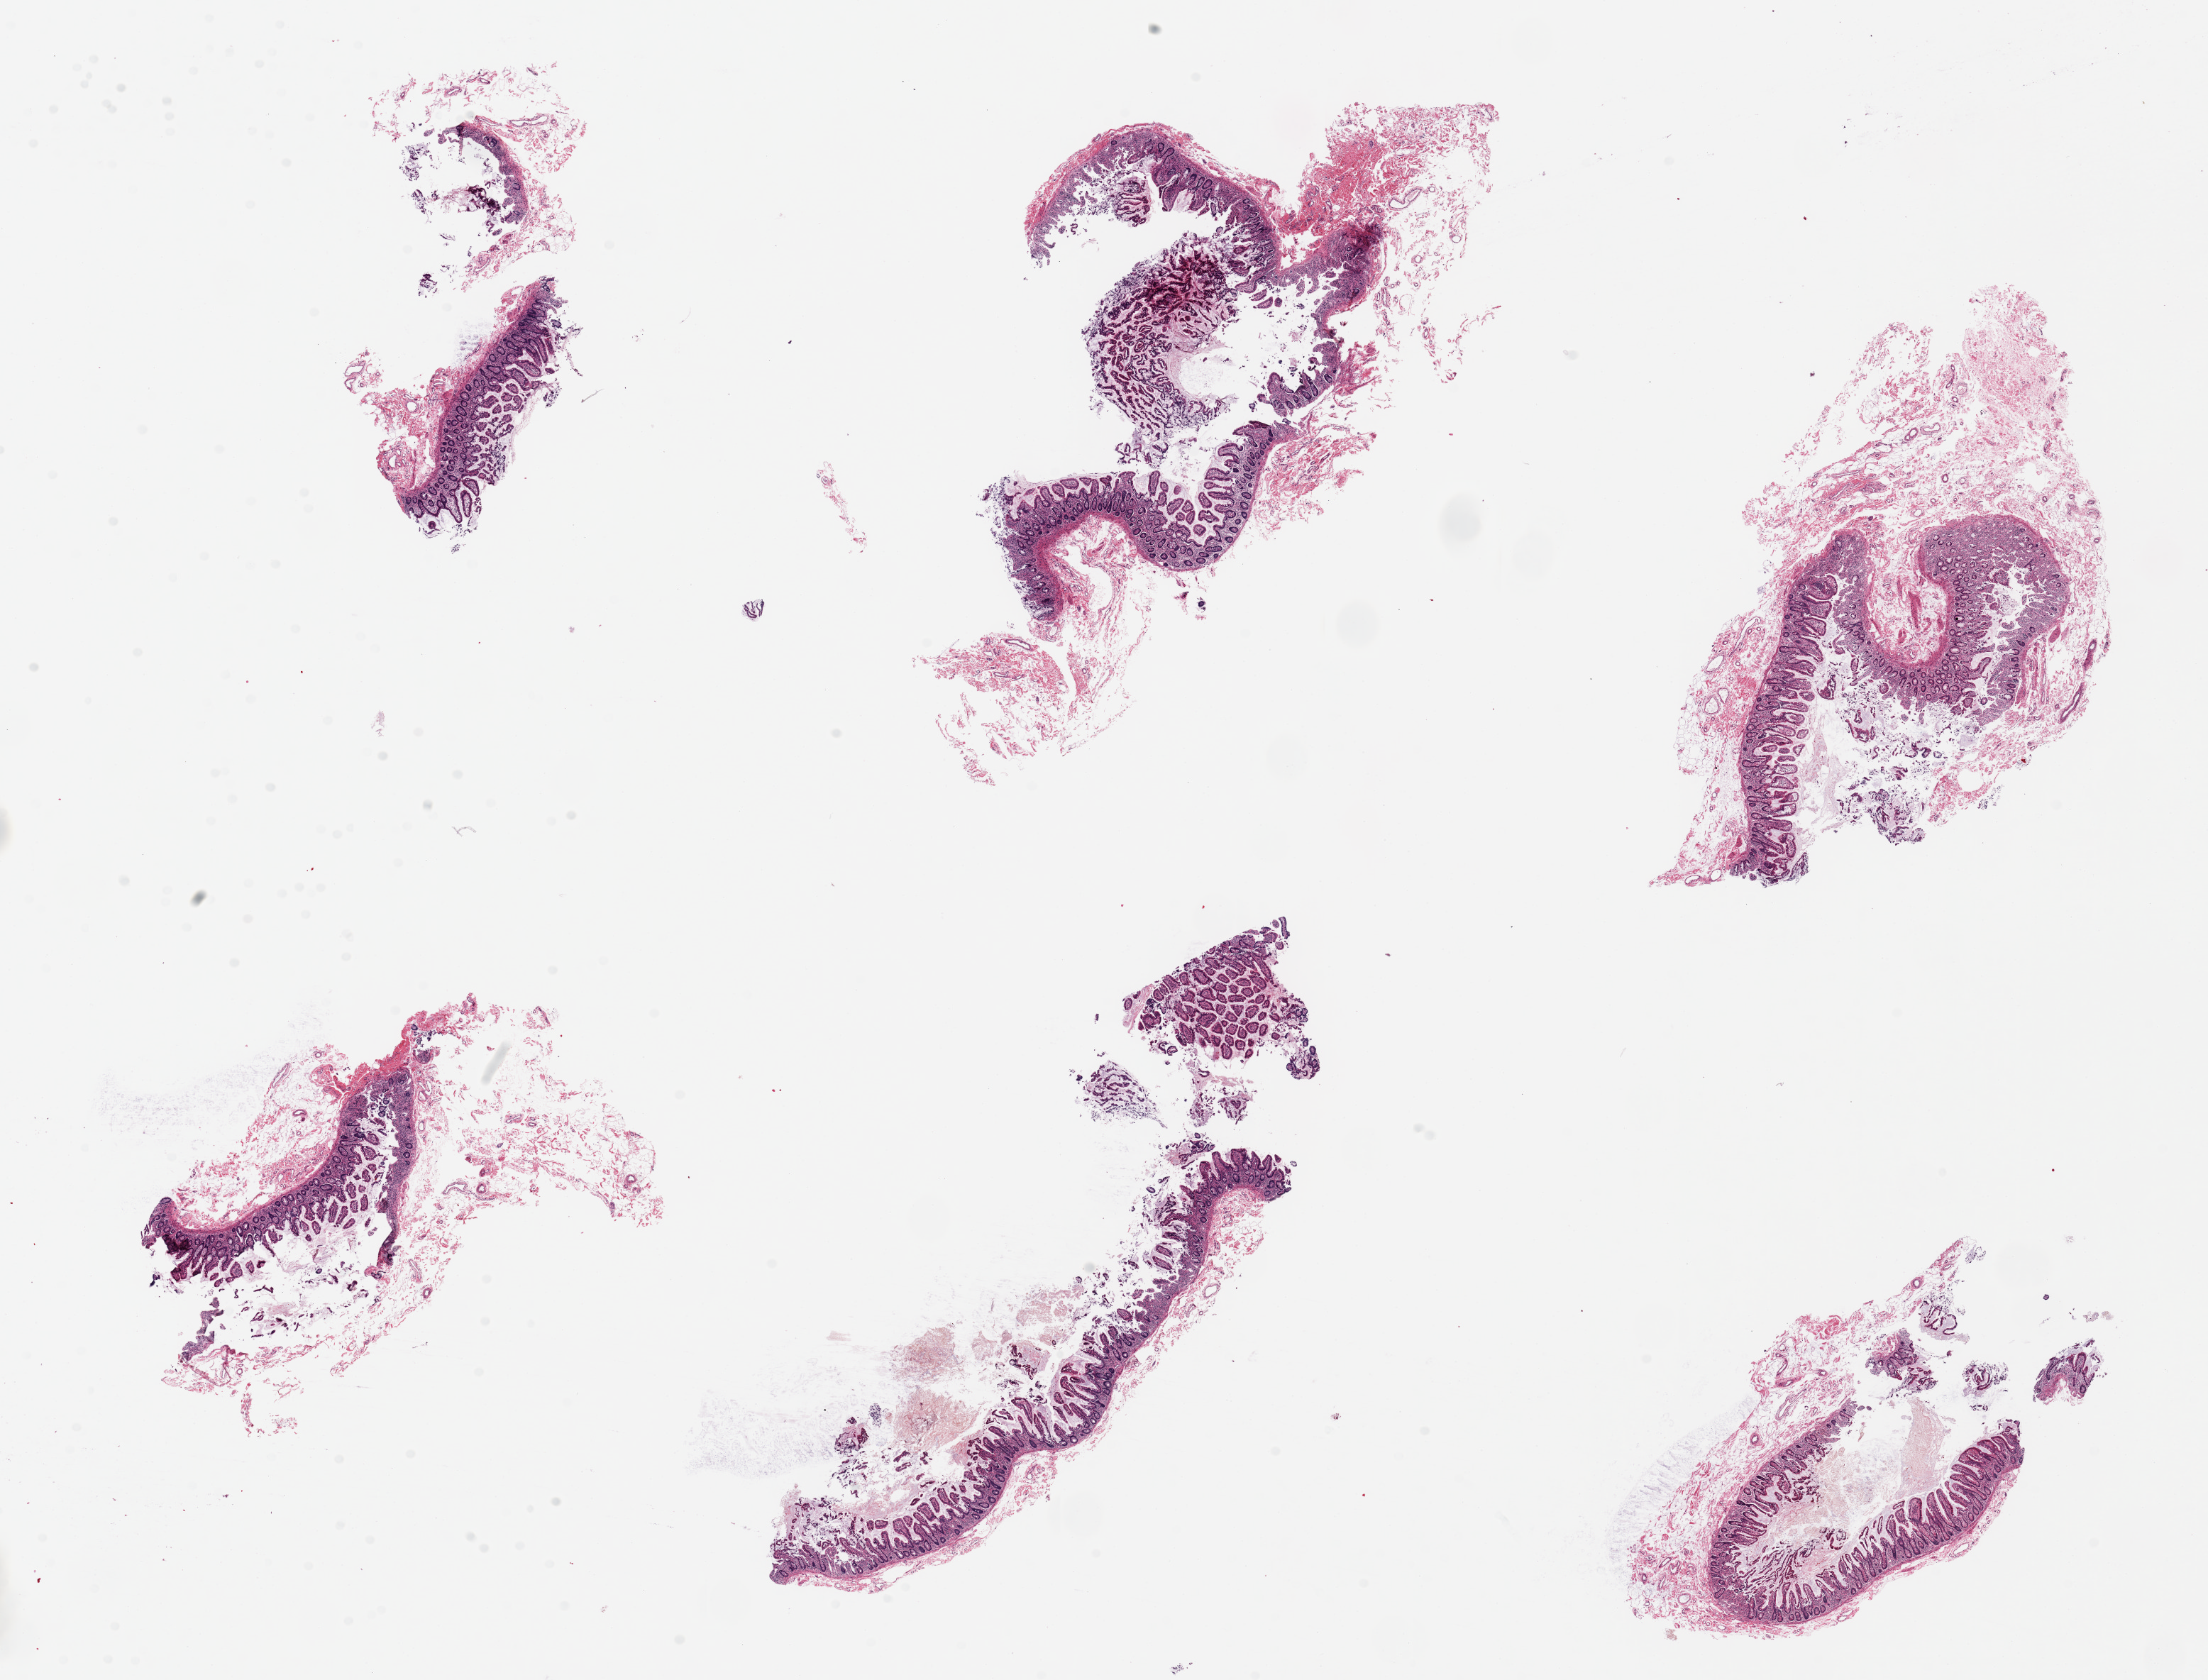
Digitized hematoxylin and eosin (H&E)-stained section, whole scanned area (about 24.6 x 18.7 mm, acquisition: 20x scan) shown as a low-resolution overview; PAXgene-fixed, paraffin-embedded tissue; section of ileum (target tissue); tissue donor sample.
- pathologist's review note for this sample: 4 pieces ~6x3mm, all mucosa,correctly collected but minimal lymphoid elements